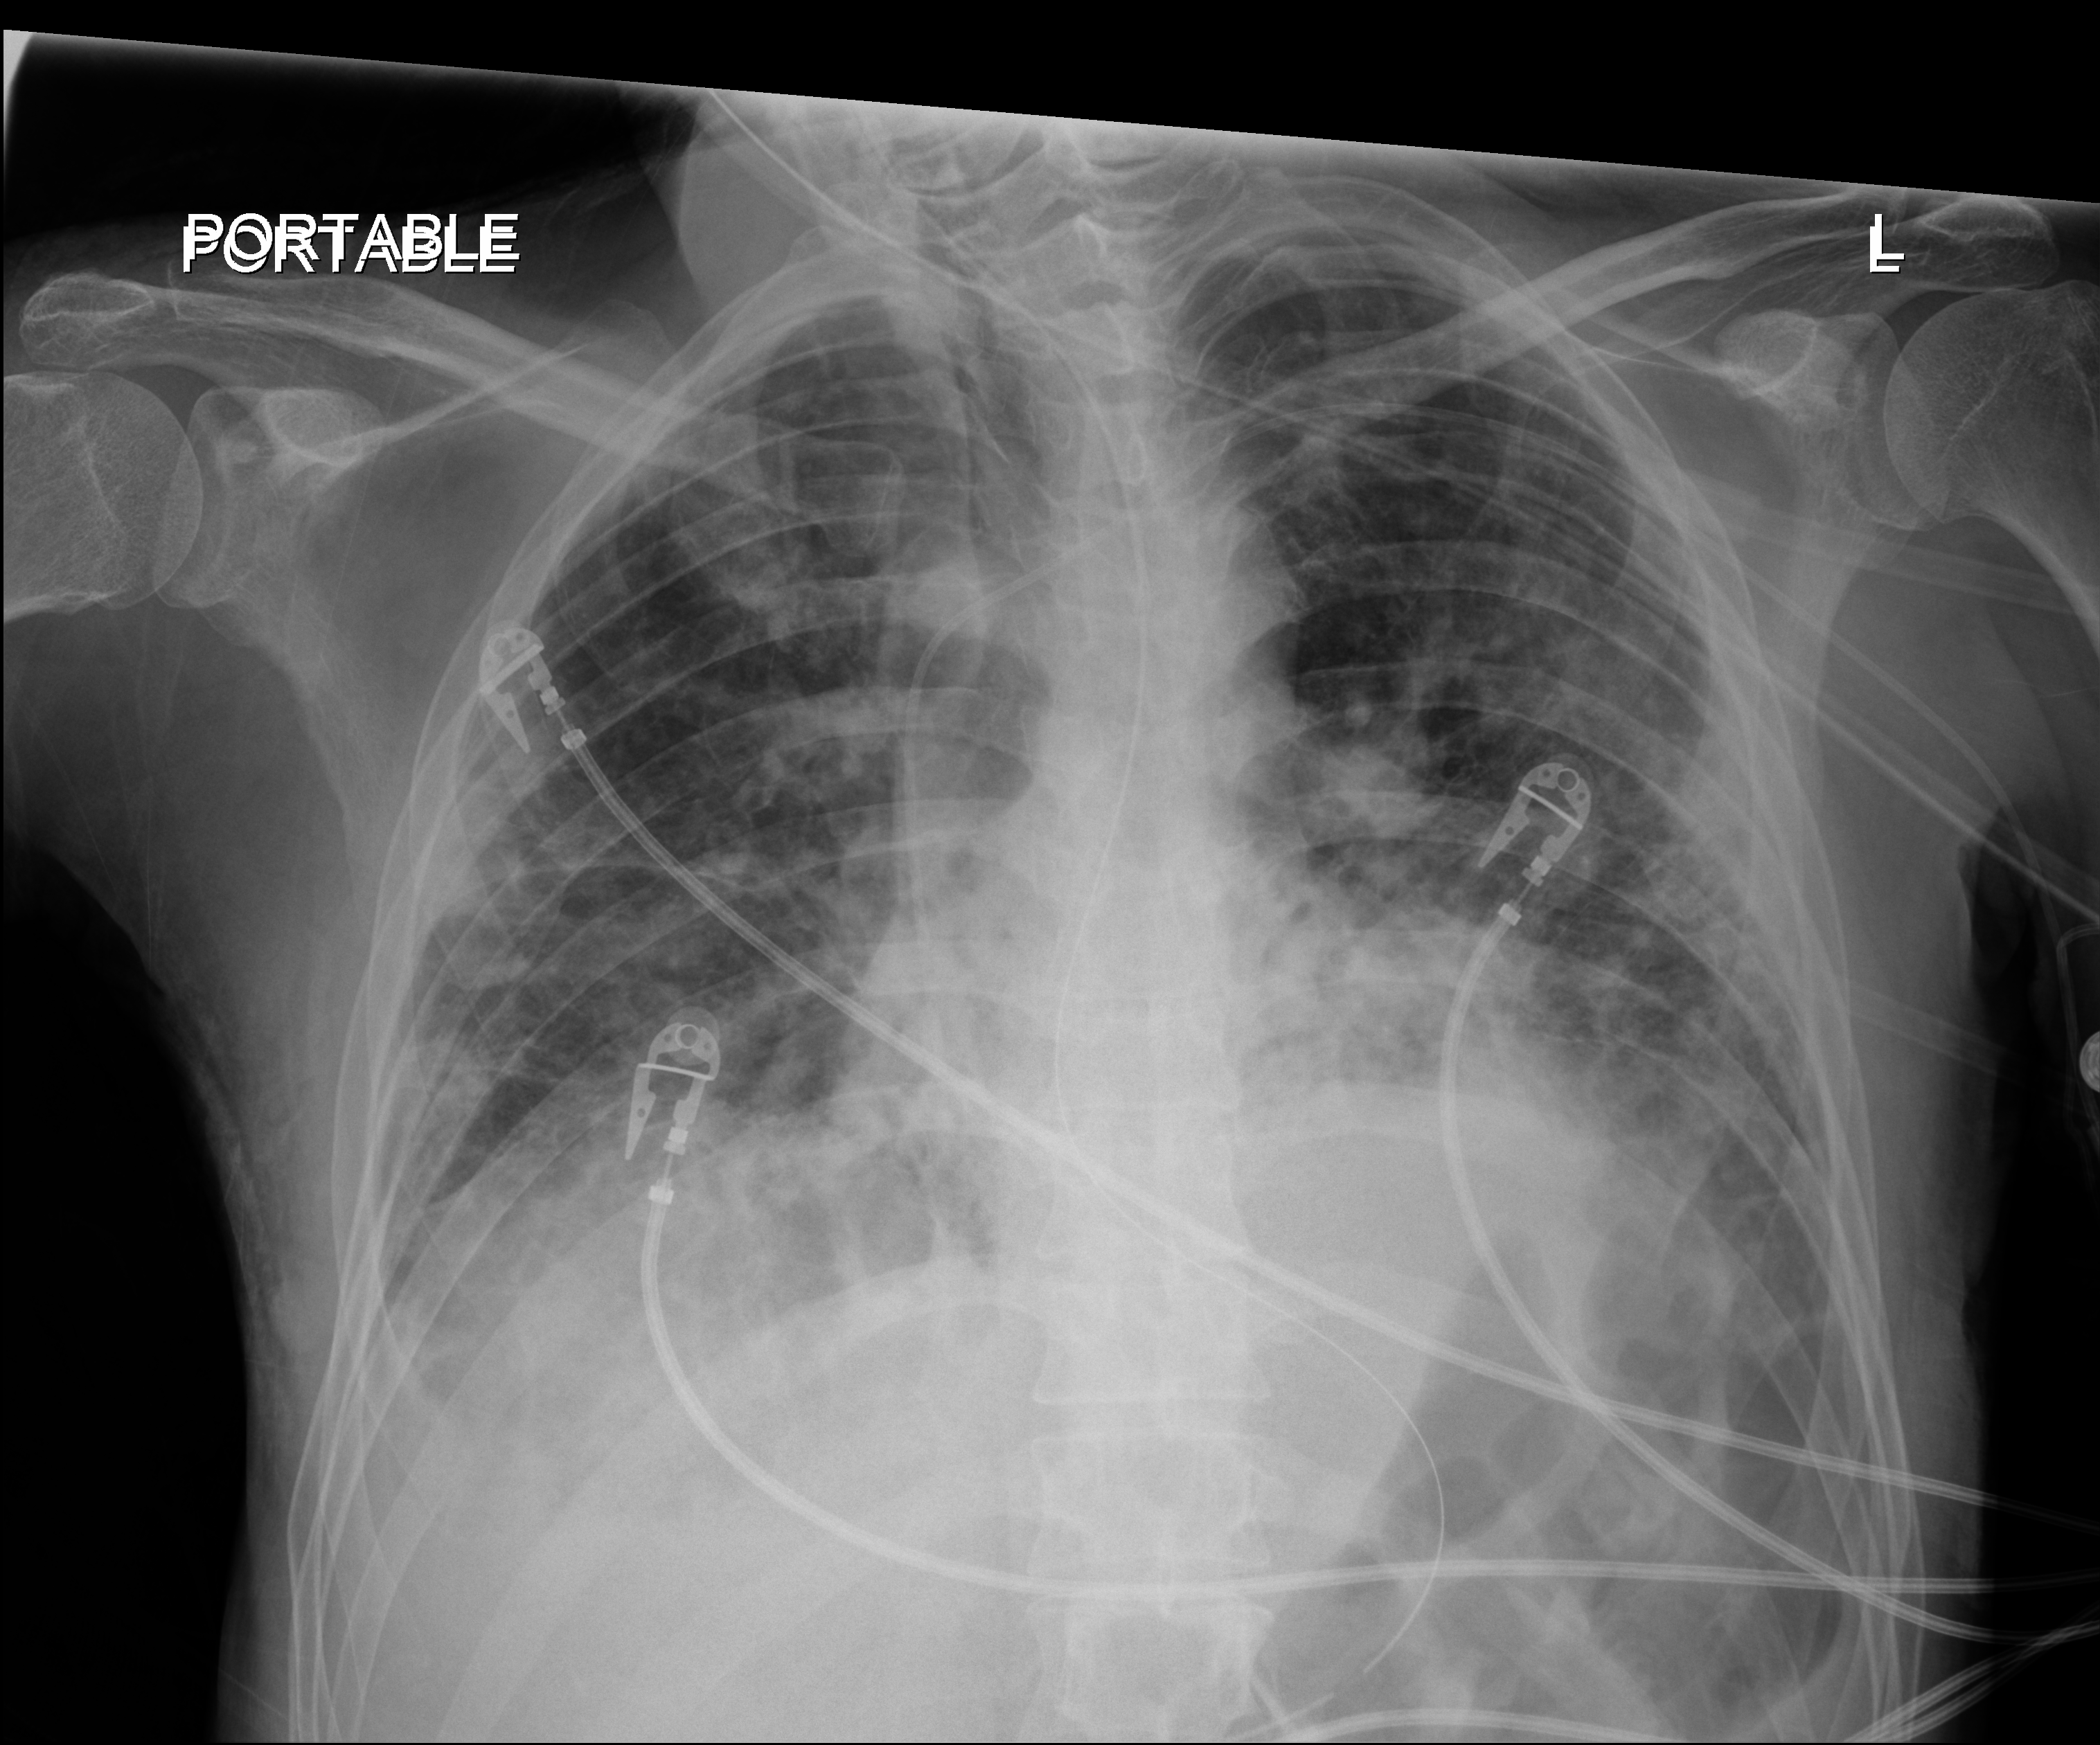
Bedside chest radiograph (digital radiography), anteroposterior (AP) projection. Male patient hospitalised with COVID-19, age 18–59 years.
From the hospital-stay record, not from the radiograph (when in the stay this image was taken is not recorded):
- admitted to intensive care during this hospital stay: yes
- other chronic lung disease (admission record): no